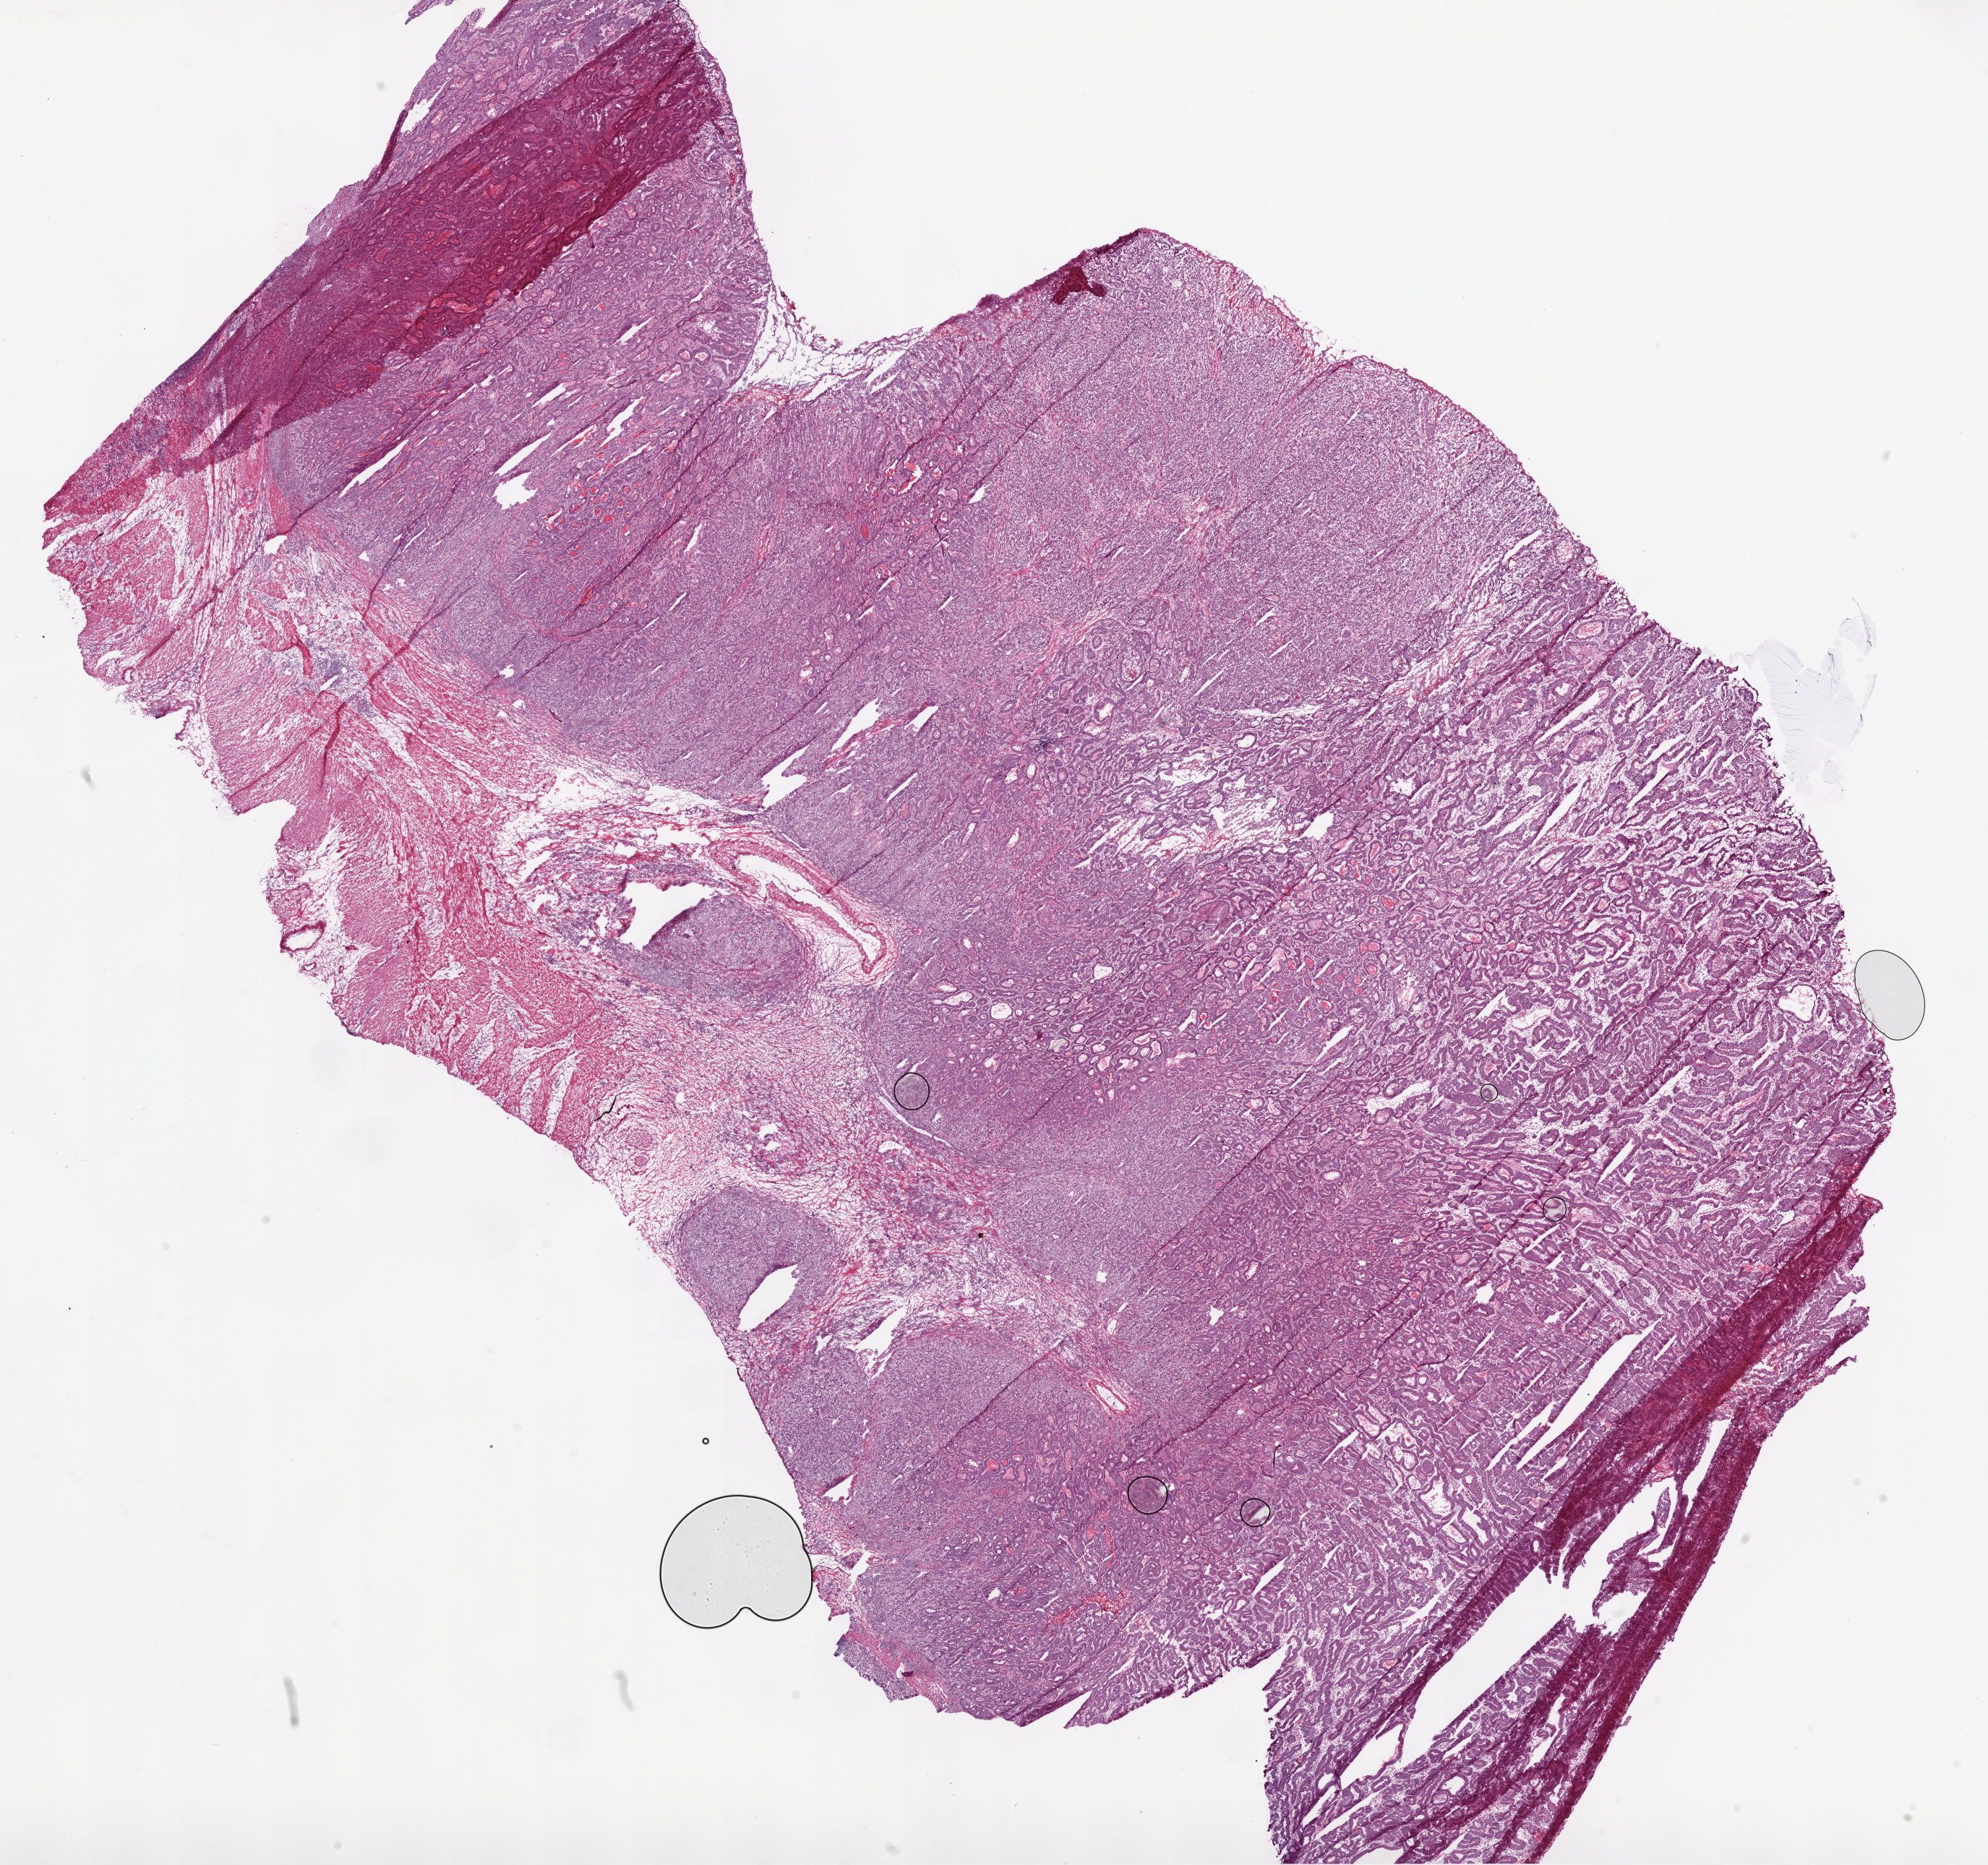
Whole-slide histology image, H&E, whole scanned area (about 22.1 x 20.7 mm) shown as a low-resolution overview, frozen section from the bottom of the tissue portion, sample: primary tumour, stomach. Patient: female, age at initial diagnosis 78 years.
Diagnosis: Adenocarcinoma, NOS.